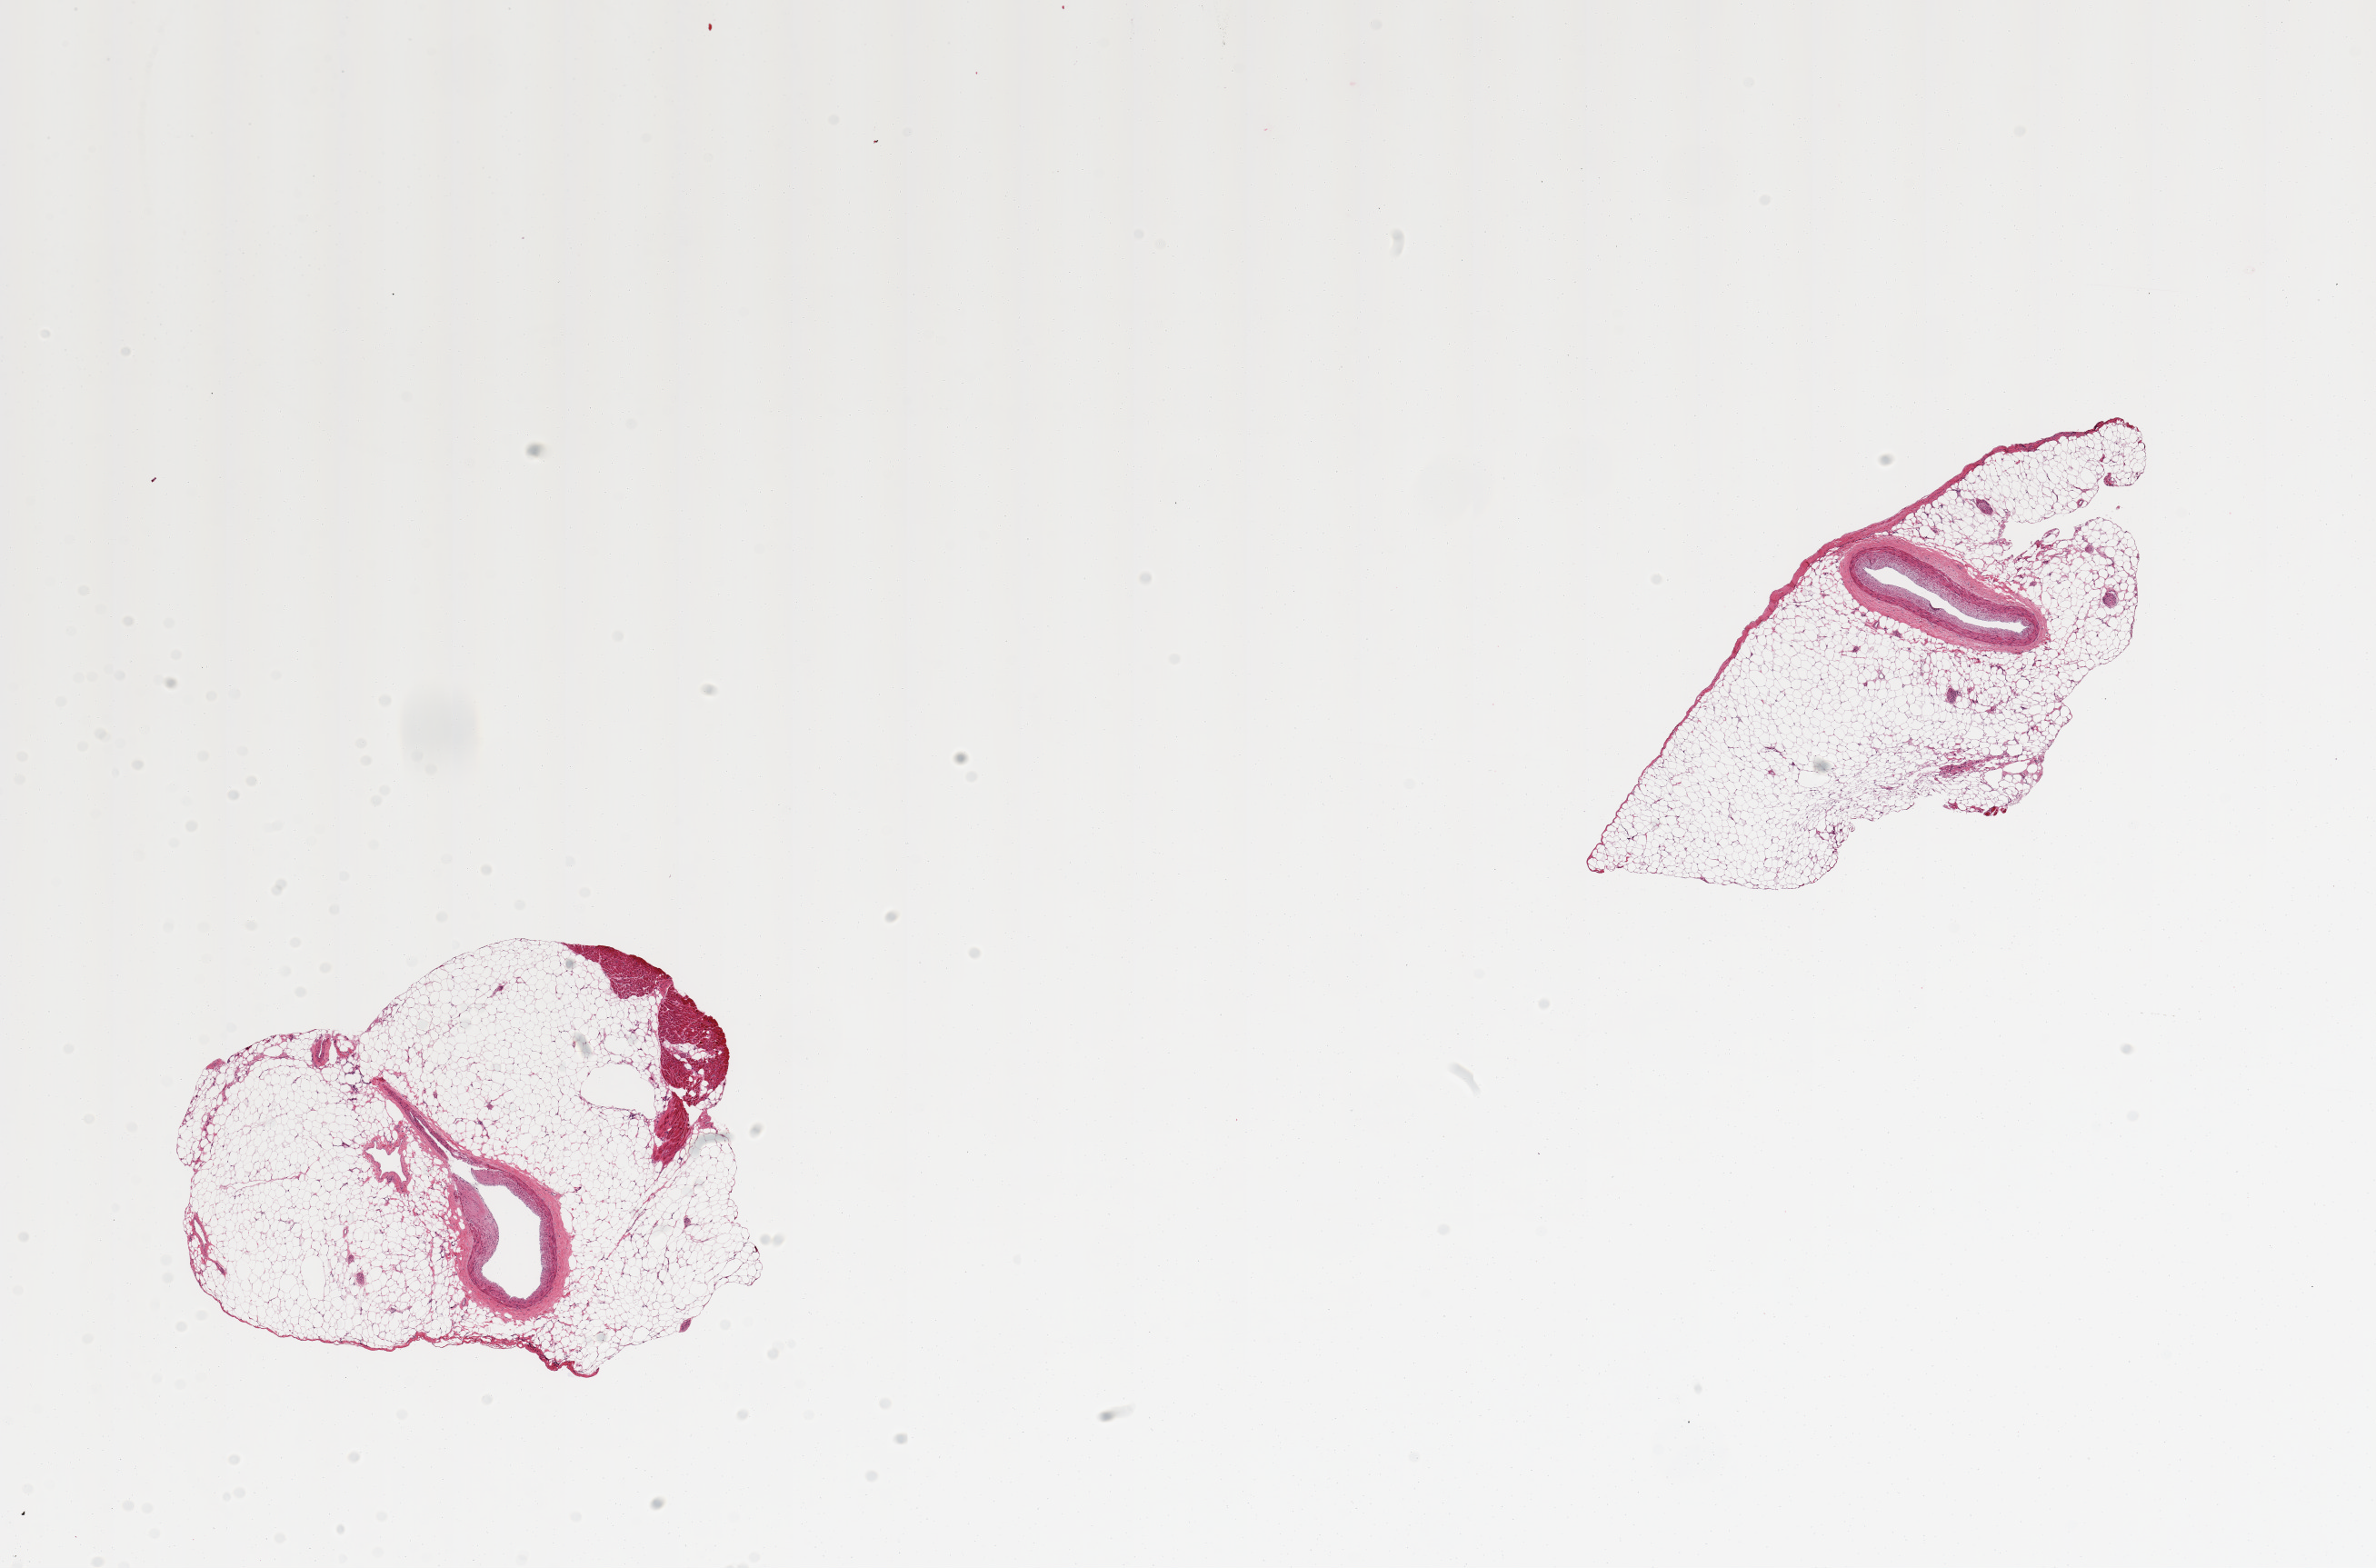
Digitized hematoxylin and eosin (H&E)-stained section, brightfield — whole scanned area (about 20.7 x 13.6 mm, from a 20x scan) shown as a low-resolution overview. PAXgene-fixed paraffin-embedded (PFPE) section. Sampled site (target tissue): coronary artery. Tissue donor sample. Donor: male.
Reviewer comment on this tissue sample: 2 ~1mm d pieces, less than 20% of aliquot; rest is fat.